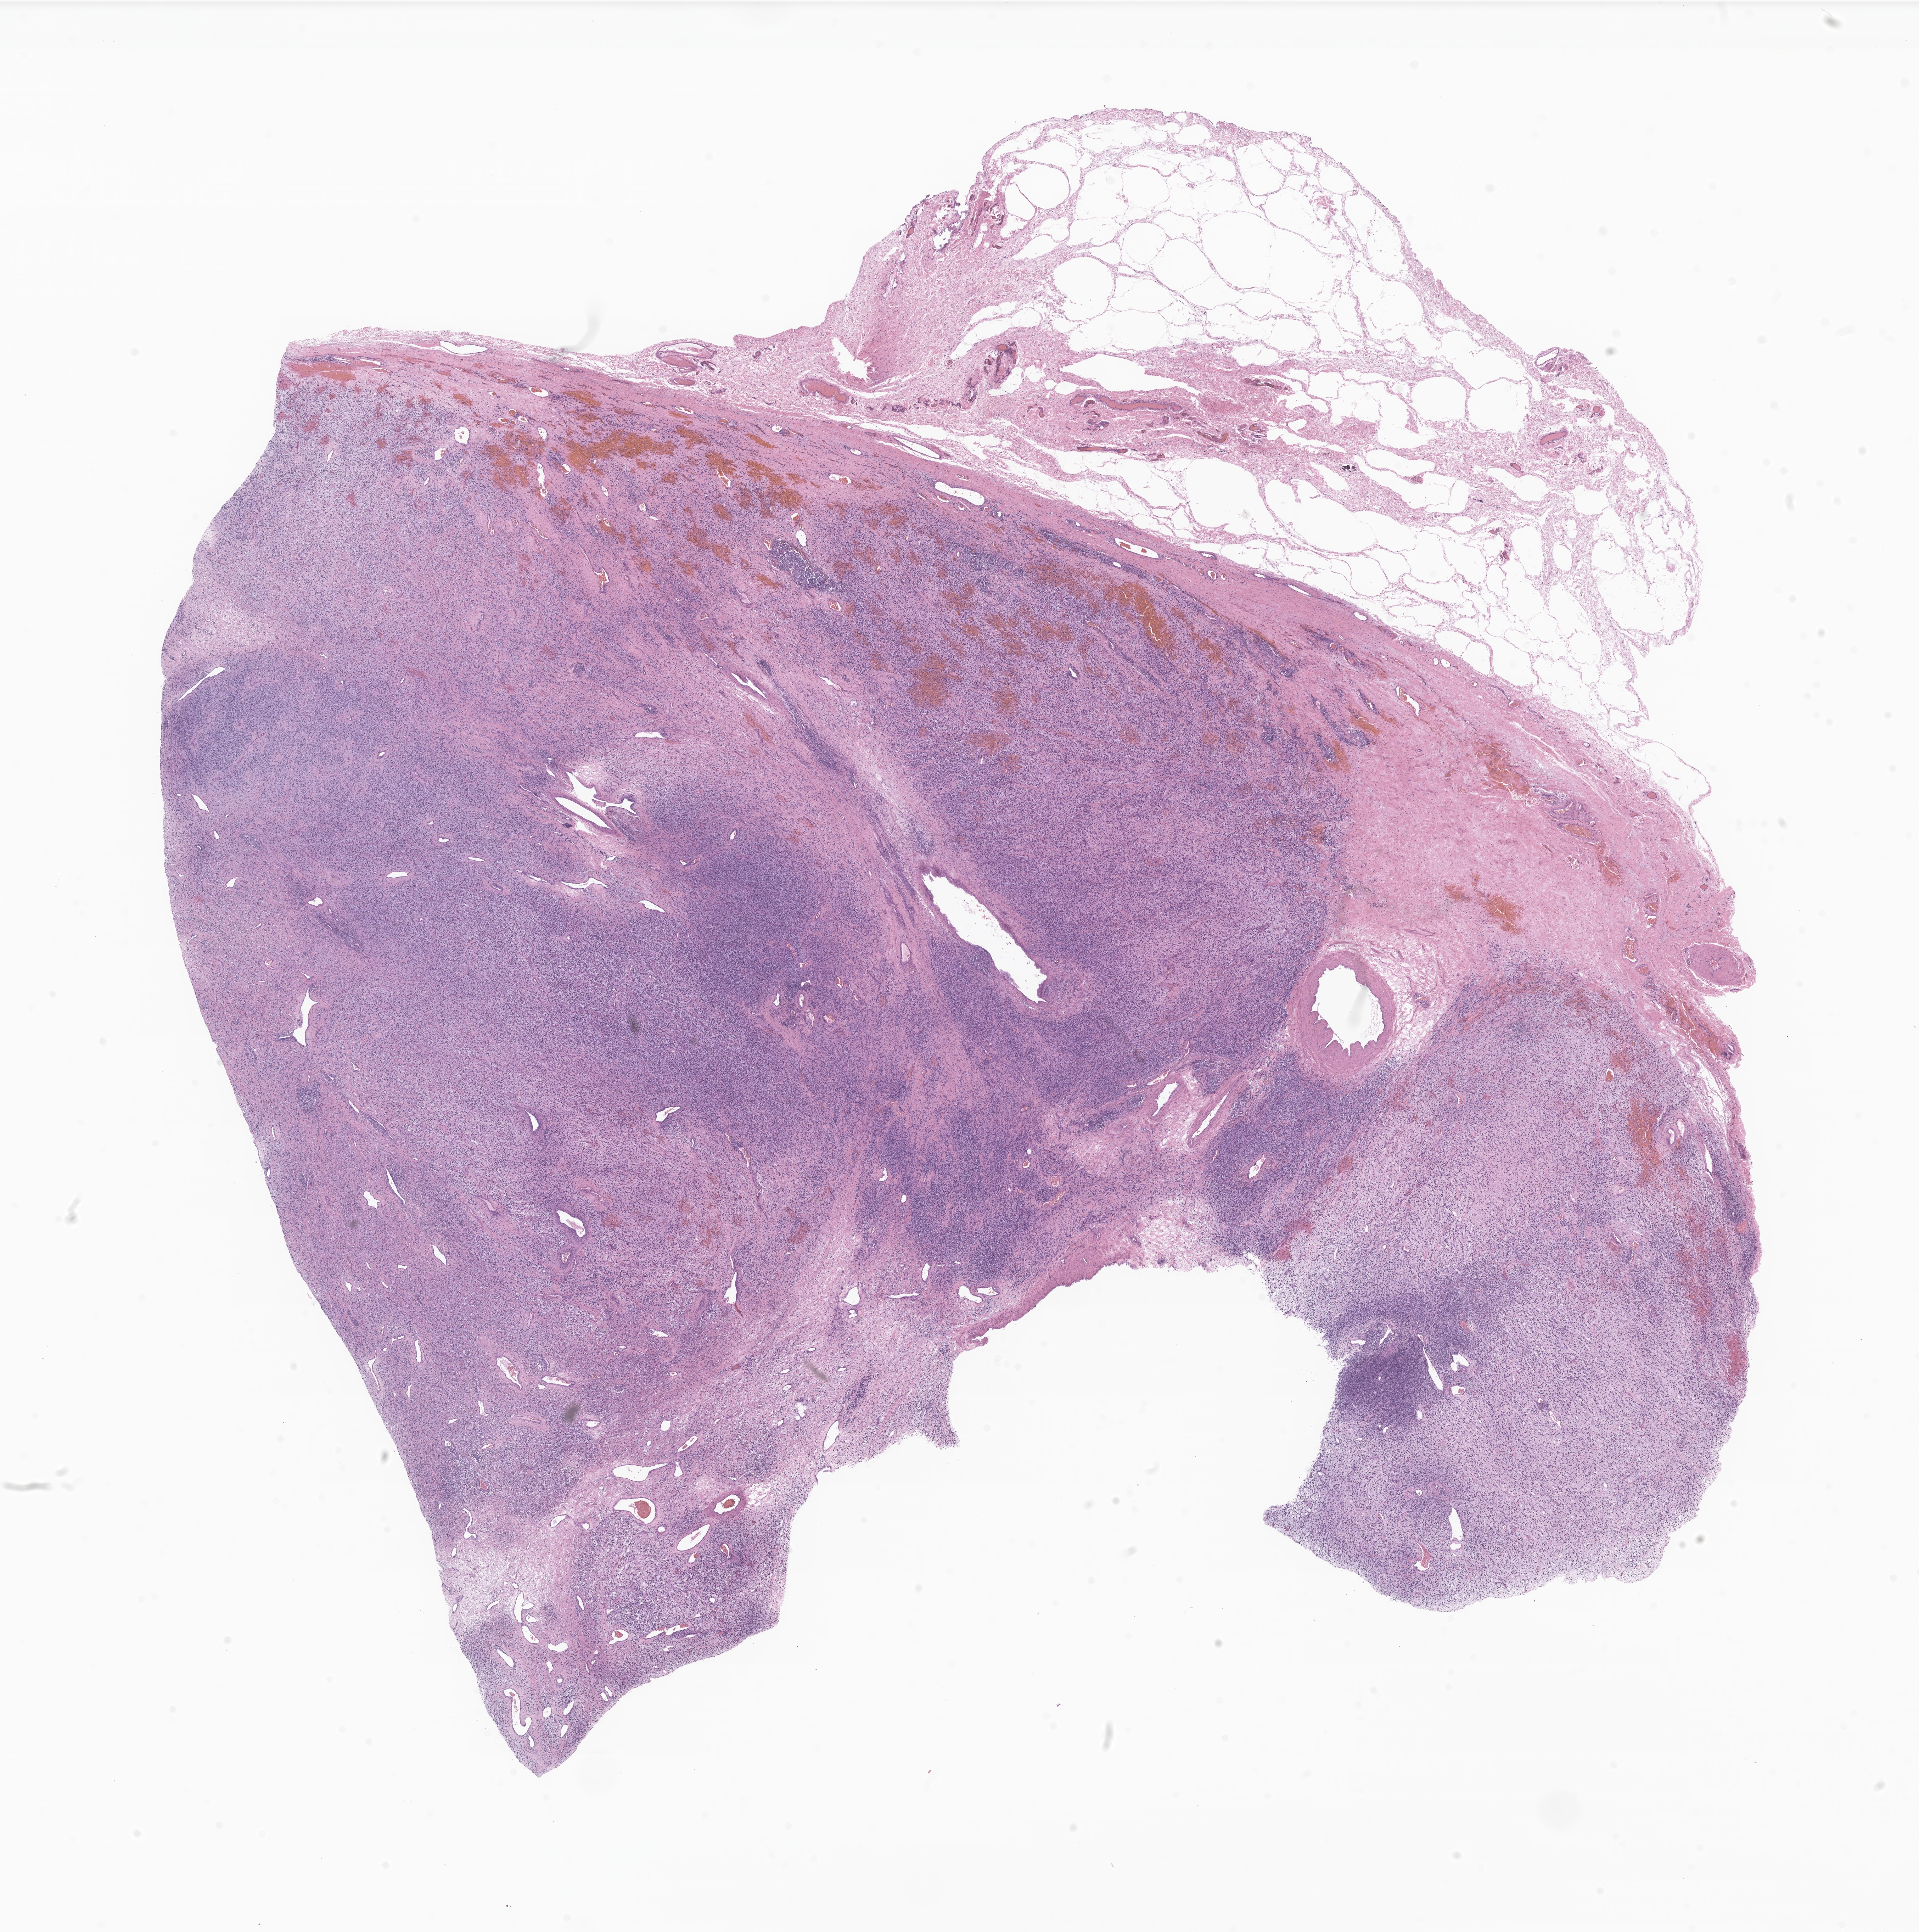
Whole-slide image, H&E stain of tumor tissue from the testis, low-resolution overview of the scanned area, about 22.8 x 23.0 mm. FFPE section. Male patient, age 205 months (17 years 1 month).
- recorded diagnosis: Rhabdomyosarcoma, NOS